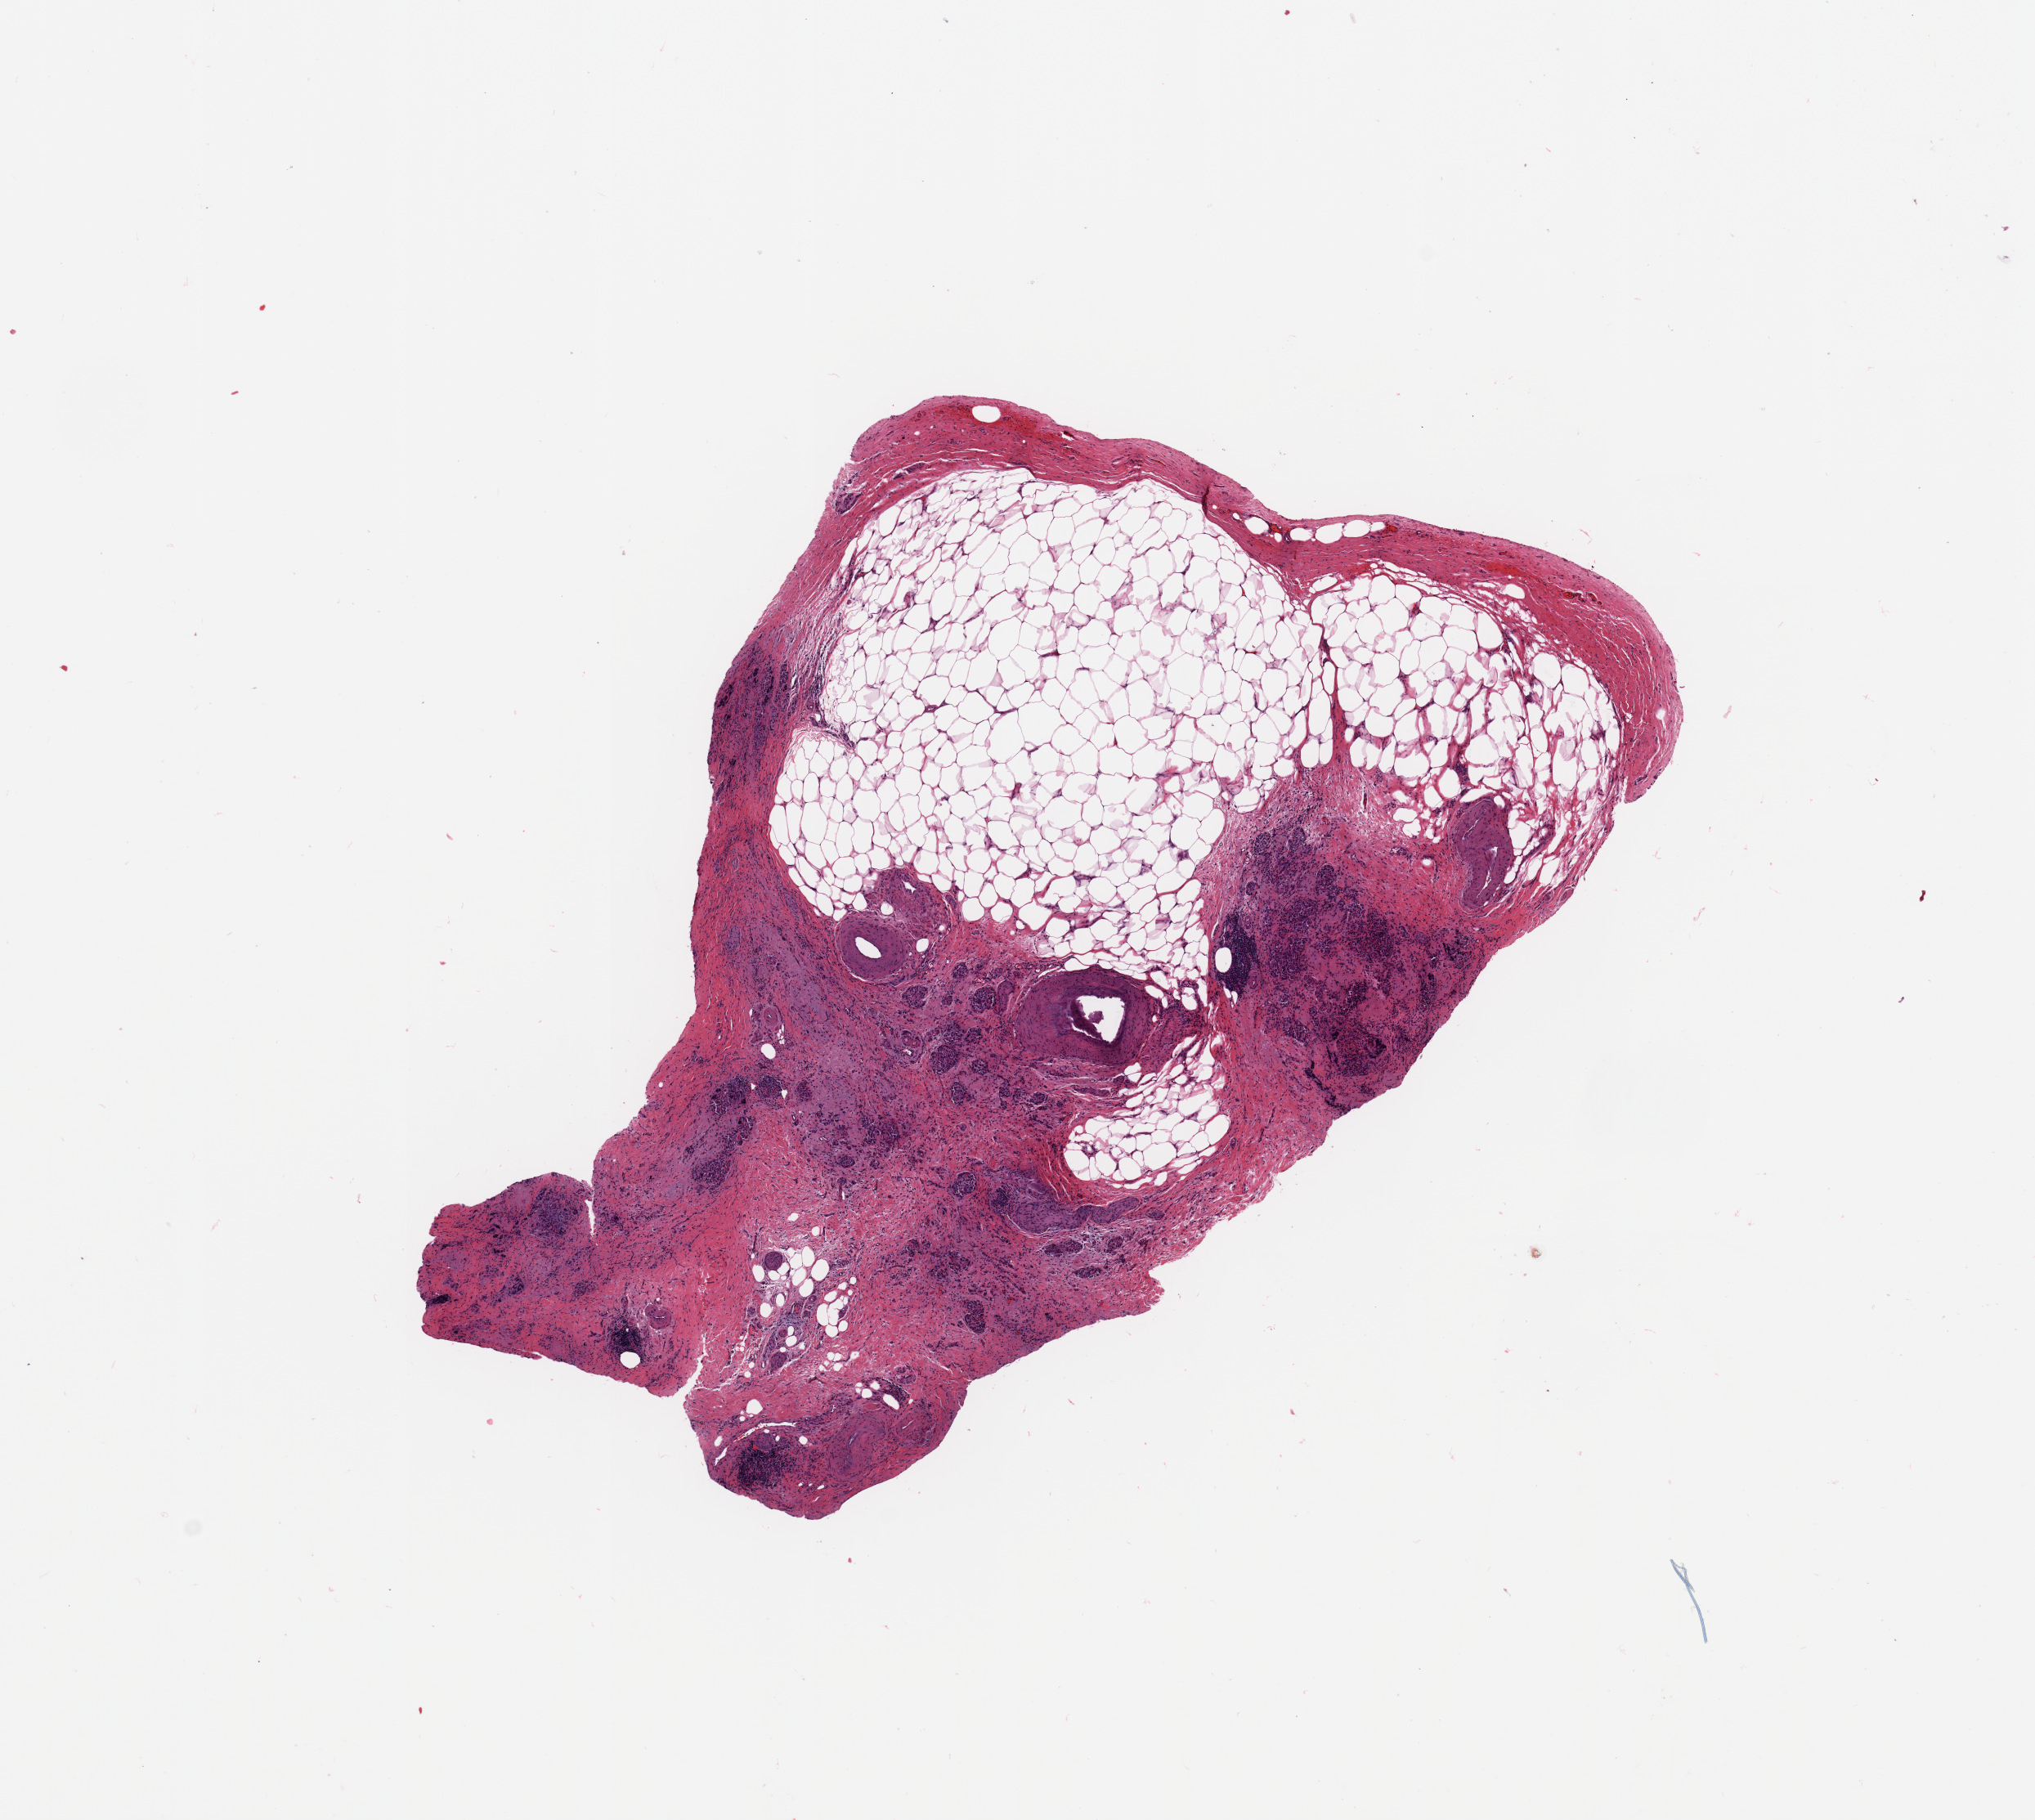
Whole-slide histology image, H&E-stained — shown as a low-resolution overview of the whole scanned area (about 9.8 x 8.8 mm, slide scanned at 20x), pancreas, normal (non-tumour) tissue. 84-year-old male patient.
This section: normal (non-tumour) tissue from the same patient. Patient diagnosis: Infiltrating duct carcinoma, NOS.